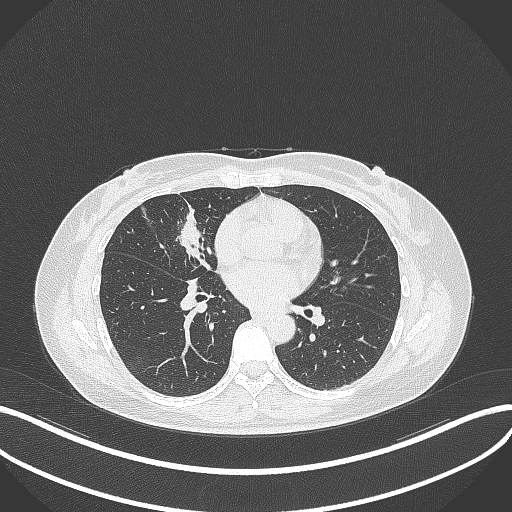
Chest CT, one axial slice; slice 141 of 284 in the series (ordered by position); 120 kVp; lung window (W 1500 / L -600 HU); 1 mm slice thickness; 512 × 512 image matrix, field of view 400 × 400 mm. Female patient, age 43 years. Case-level facts recorded for this patient, not image findings: clinical TNM (as recorded): T1c N3 M1.
Outlined on this slice (bounding box drawn by a radiologist):
- lung tumour (recorded histology: adenocarcinoma): bounding box [x1, y1, x2, y2] px = [169, 205, 208, 268]